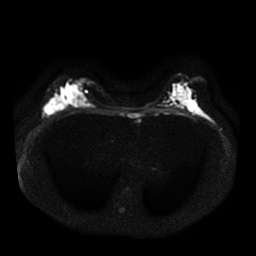
Breast MRI, one axial slice. Diffusion-weighted series; image 2 of 4 stored at this slice position (different b-values; order by instance number). 1.5 T. 5 mm slice thickness. 256 × 256 image matrix. Female patient.
Annotated regions visible in this slice (outlined manually by an expert reader):
- tumour on diffusion-weighted imaging: bounding box (x1, y1, x2, y2) in pixels: (44, 104, 54, 114)